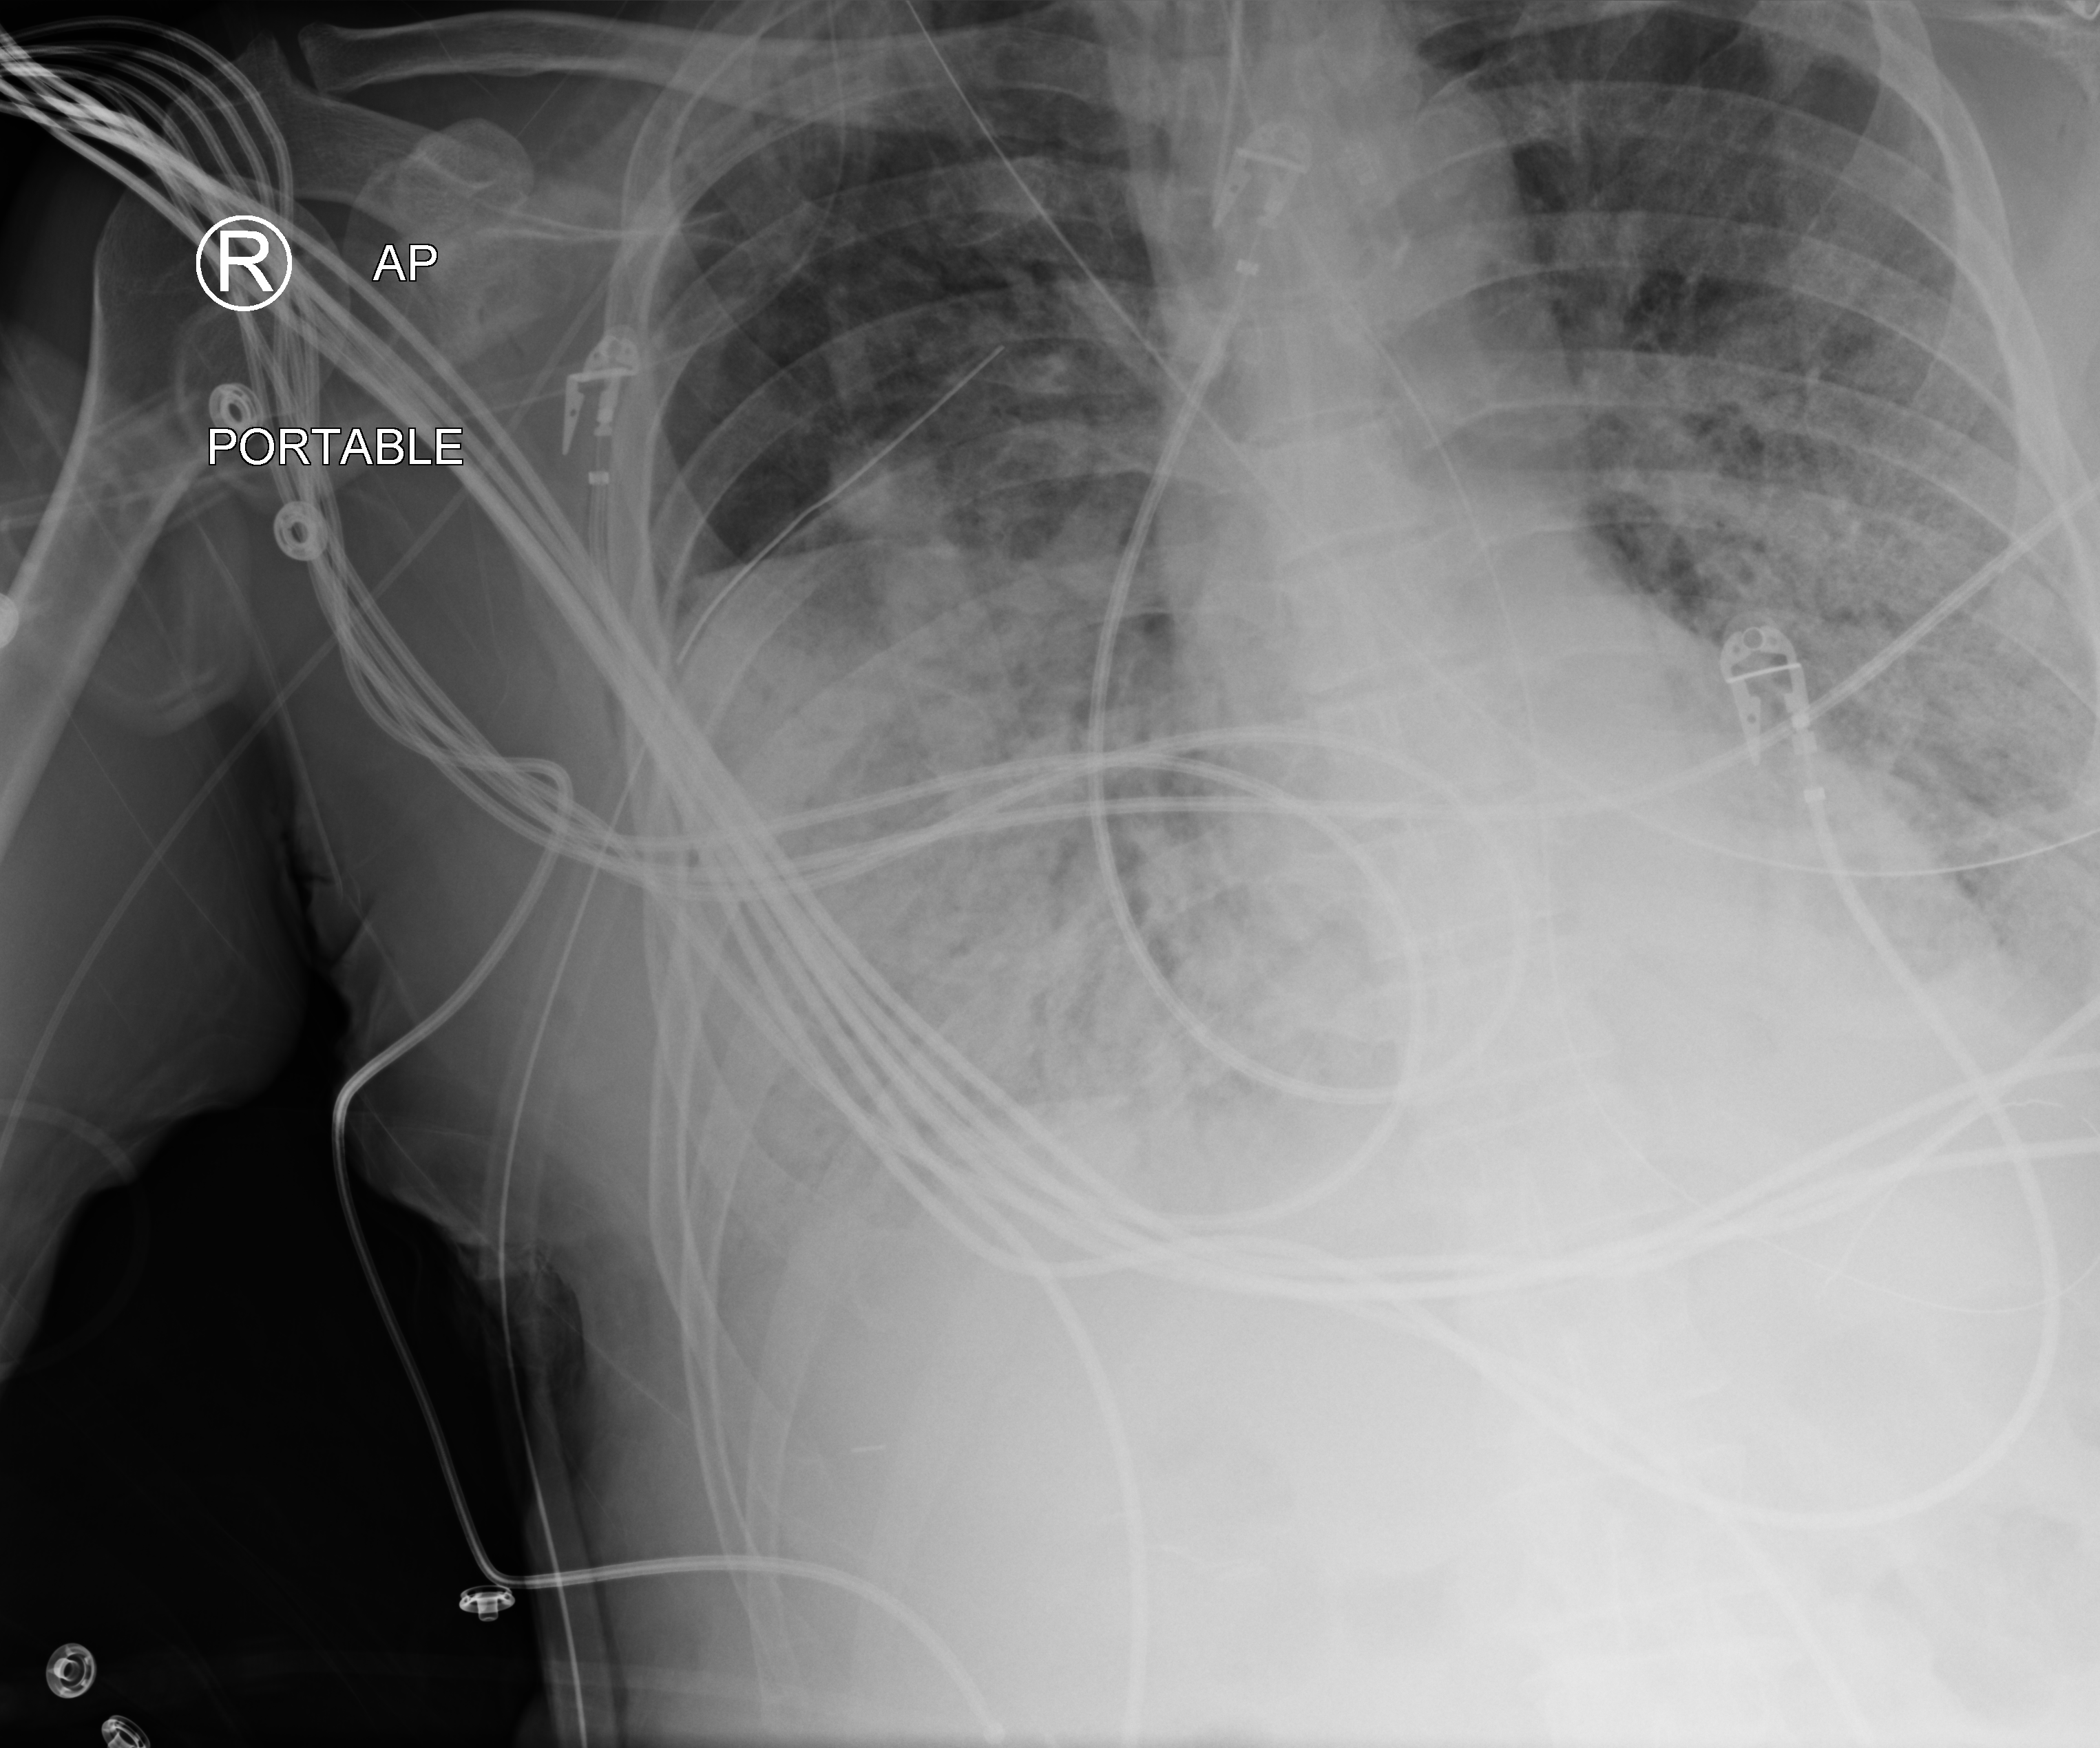
Bedside chest radiograph (computed radiography); anteroposterior (AP) projection. Male patient hospitalised with COVID-19, age 60–74 years.
From the hospital-stay record, not from the radiograph (when in the stay this image was taken is not recorded): other chronic lung disease (admission record): no.